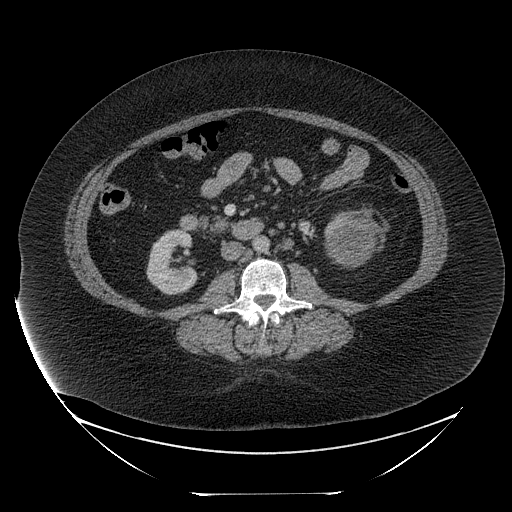
Contrast-enhanced abdominal CT, one axial slice. Slice 111 of 205 in the series (ordered by position). Reconstruction kernel STANDARD. 120 kVp. Intravenous contrast given. Soft-tissue window (W 400 / L 40 HU). 512 × 512 image matrix, field of view 500 × 500 mm. Patient: female, 53 years. Case-level facts recorded for this patient, not image findings: diagnosis: adrenocortical carcinoma; tumour side: left adrenal; tumour size at pathology: 17 cm; Ki-67 index: 20 %; stage (as recorded): 3.
Structures marked on this image (semi-automatic segmentation, software-assisted and operator-edited):
- mass: bounding box (x1, y1, x2, y2) in pixels: (329, 211, 375, 266)